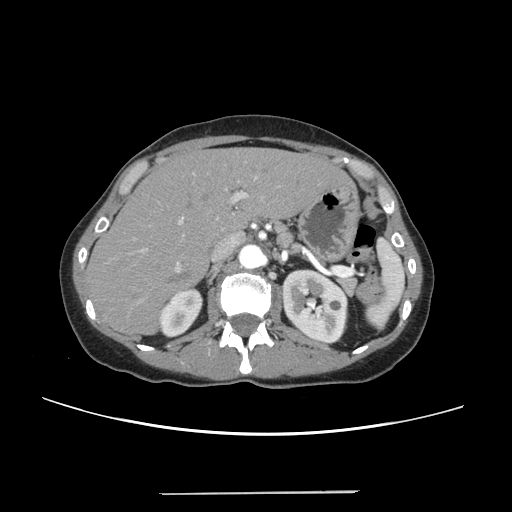
Contrast-enhanced abdominal CT, one axial slice; 120 kVp; soft-tissue window (W 400 / L 40 HU); 1.25 mm slice thickness; 512 × 512 image matrix, field of view 371 × 371 mm. Female patient, age 60 years. Case-level facts recorded for this patient, not image findings: diagnosis: colorectal cancer liver metastases, imaged before liver resection; multiple liver metastases: no; largest metastasis: 1.5 cm; disease in both lobes: no.
Annotated regions visible in this slice (outlined manually by an expert reader):
- liver: bounding box (x1, y1, x2, y2) in pixels: (88, 148, 348, 334)
- planned liver remnant (the part of the liver to remain after resection): (88, 148, 347, 334)
- portal vein (with intrahepatic branches): (138, 171, 259, 272)